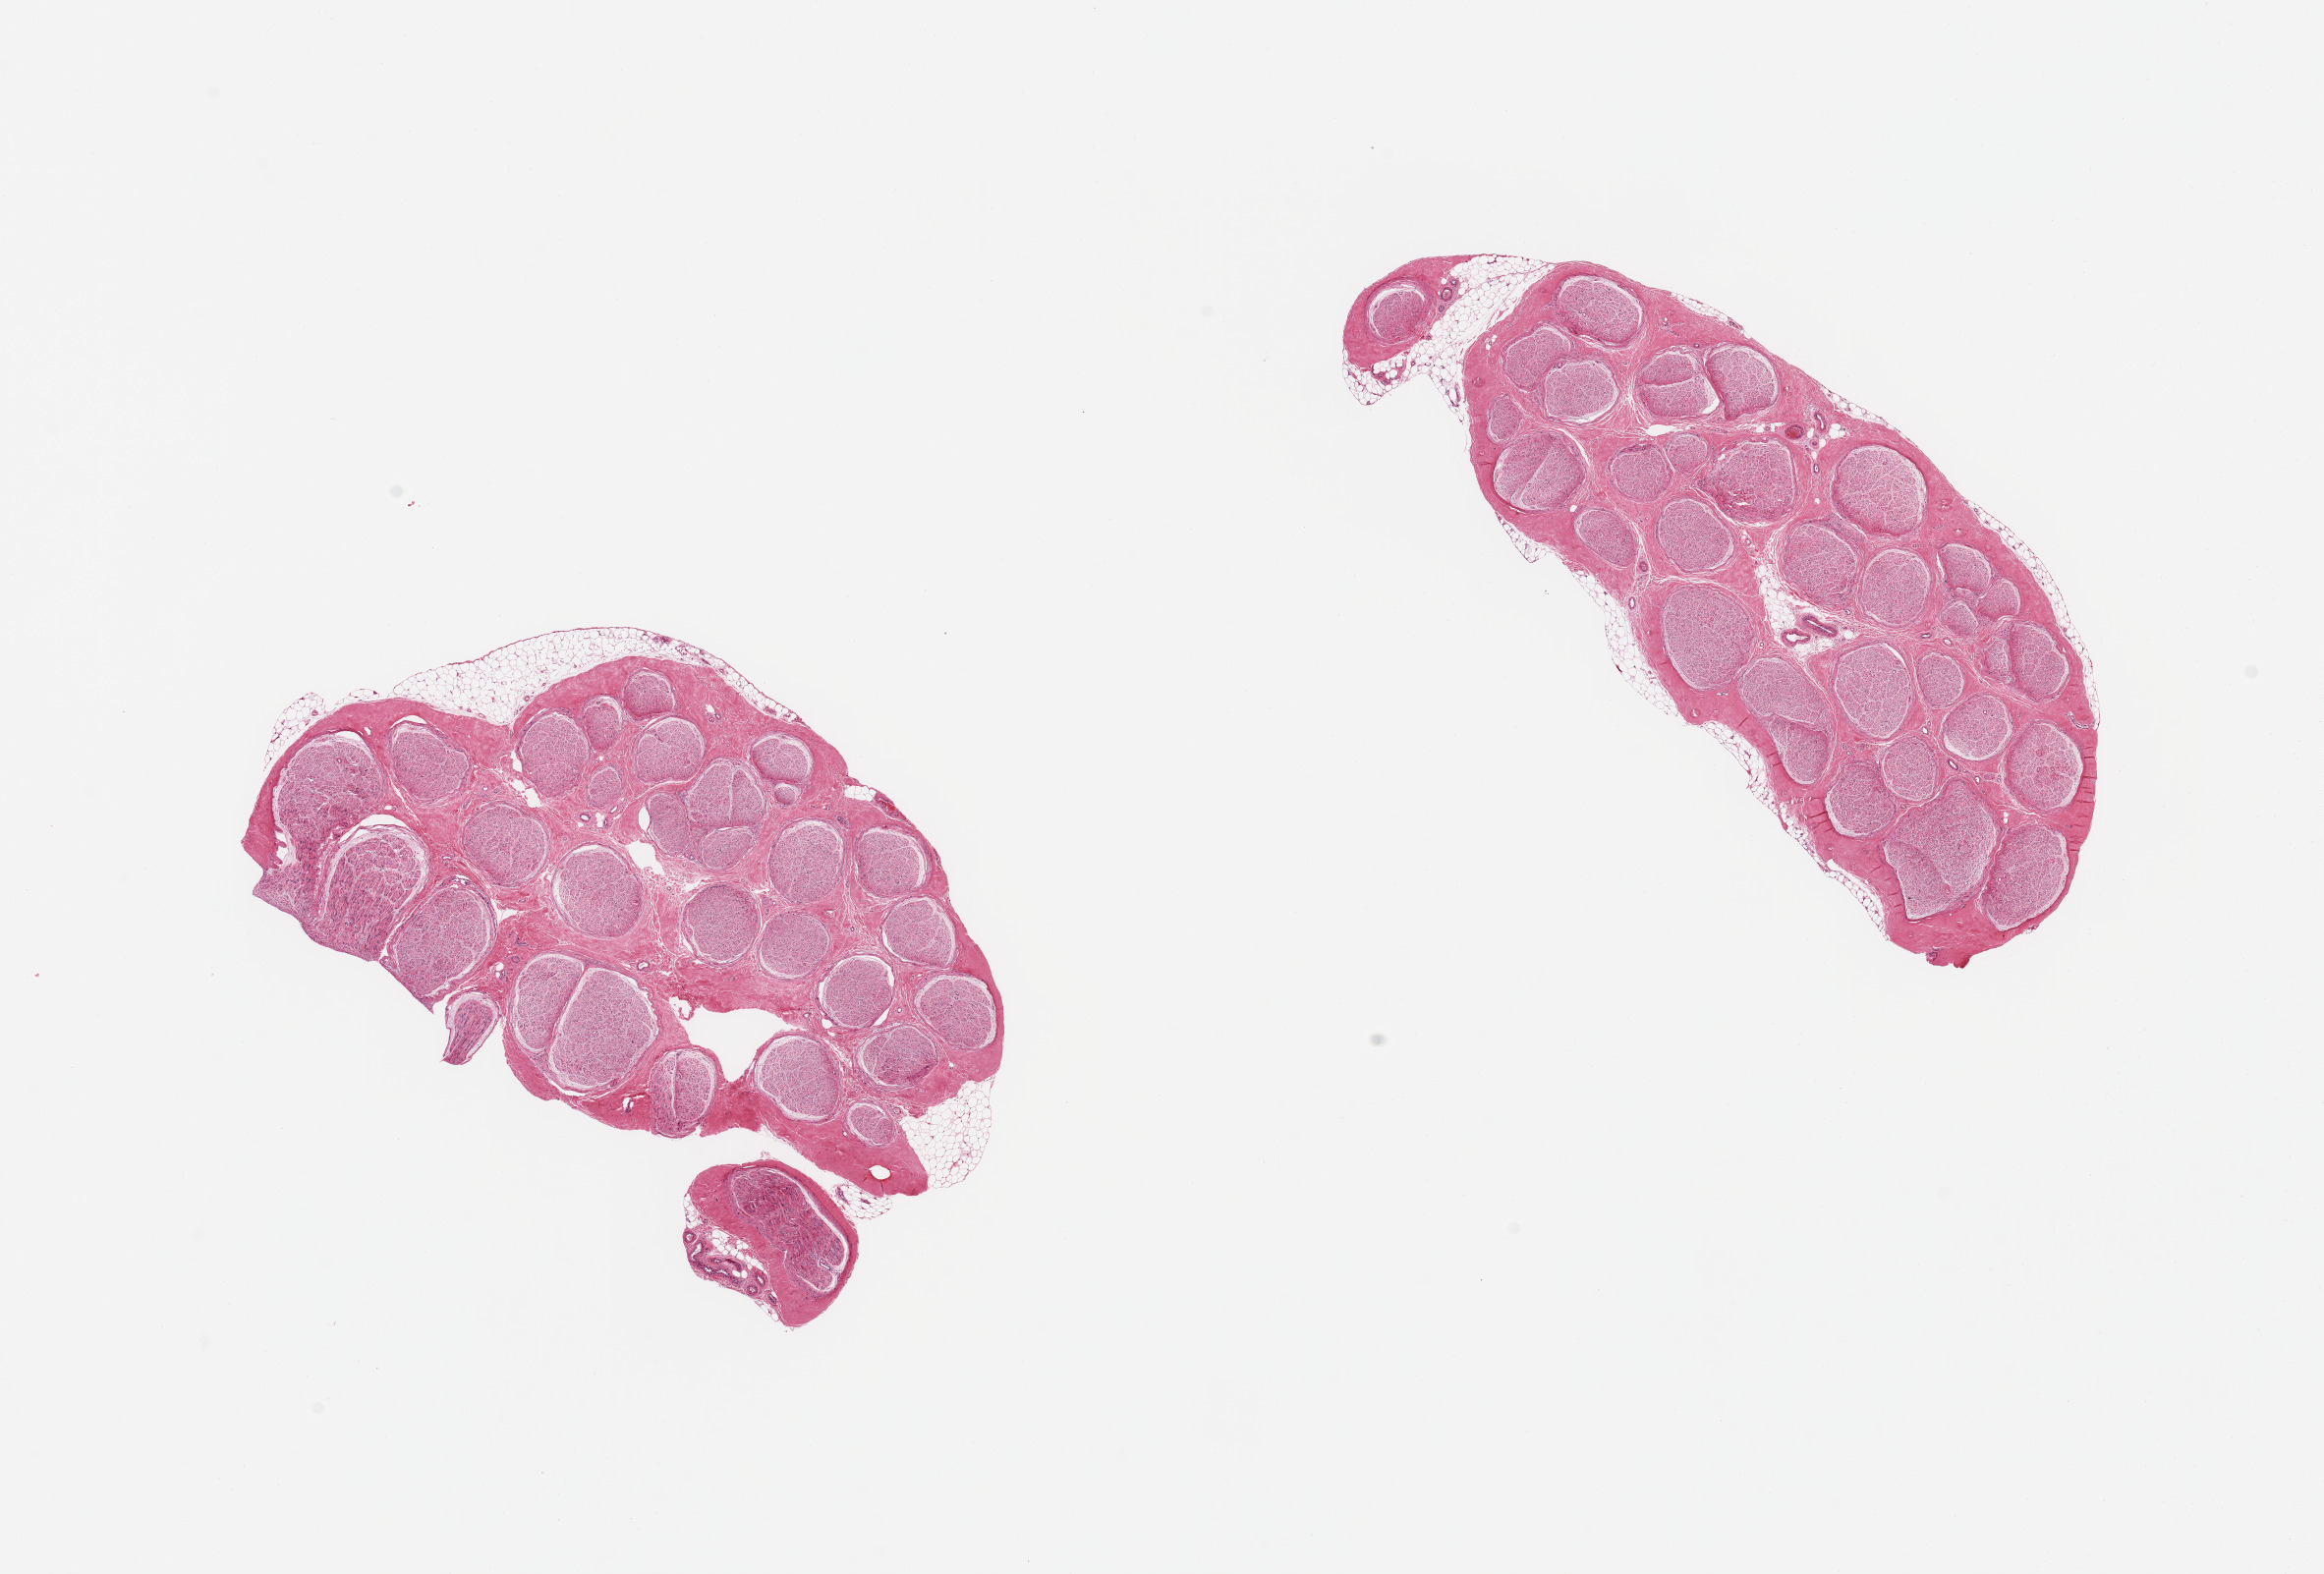
H&E whole-slide image, a low-resolution overview of the entire scanned area, about 18.7 x 12.7 mm, PAXgene-fixed, paraffin-embedded tissue, target tissue: tibial nerve, tissue donor sample. Donor: male.
• reviewer comment on this tissue sample: 2 pieces; small amounts of external fat